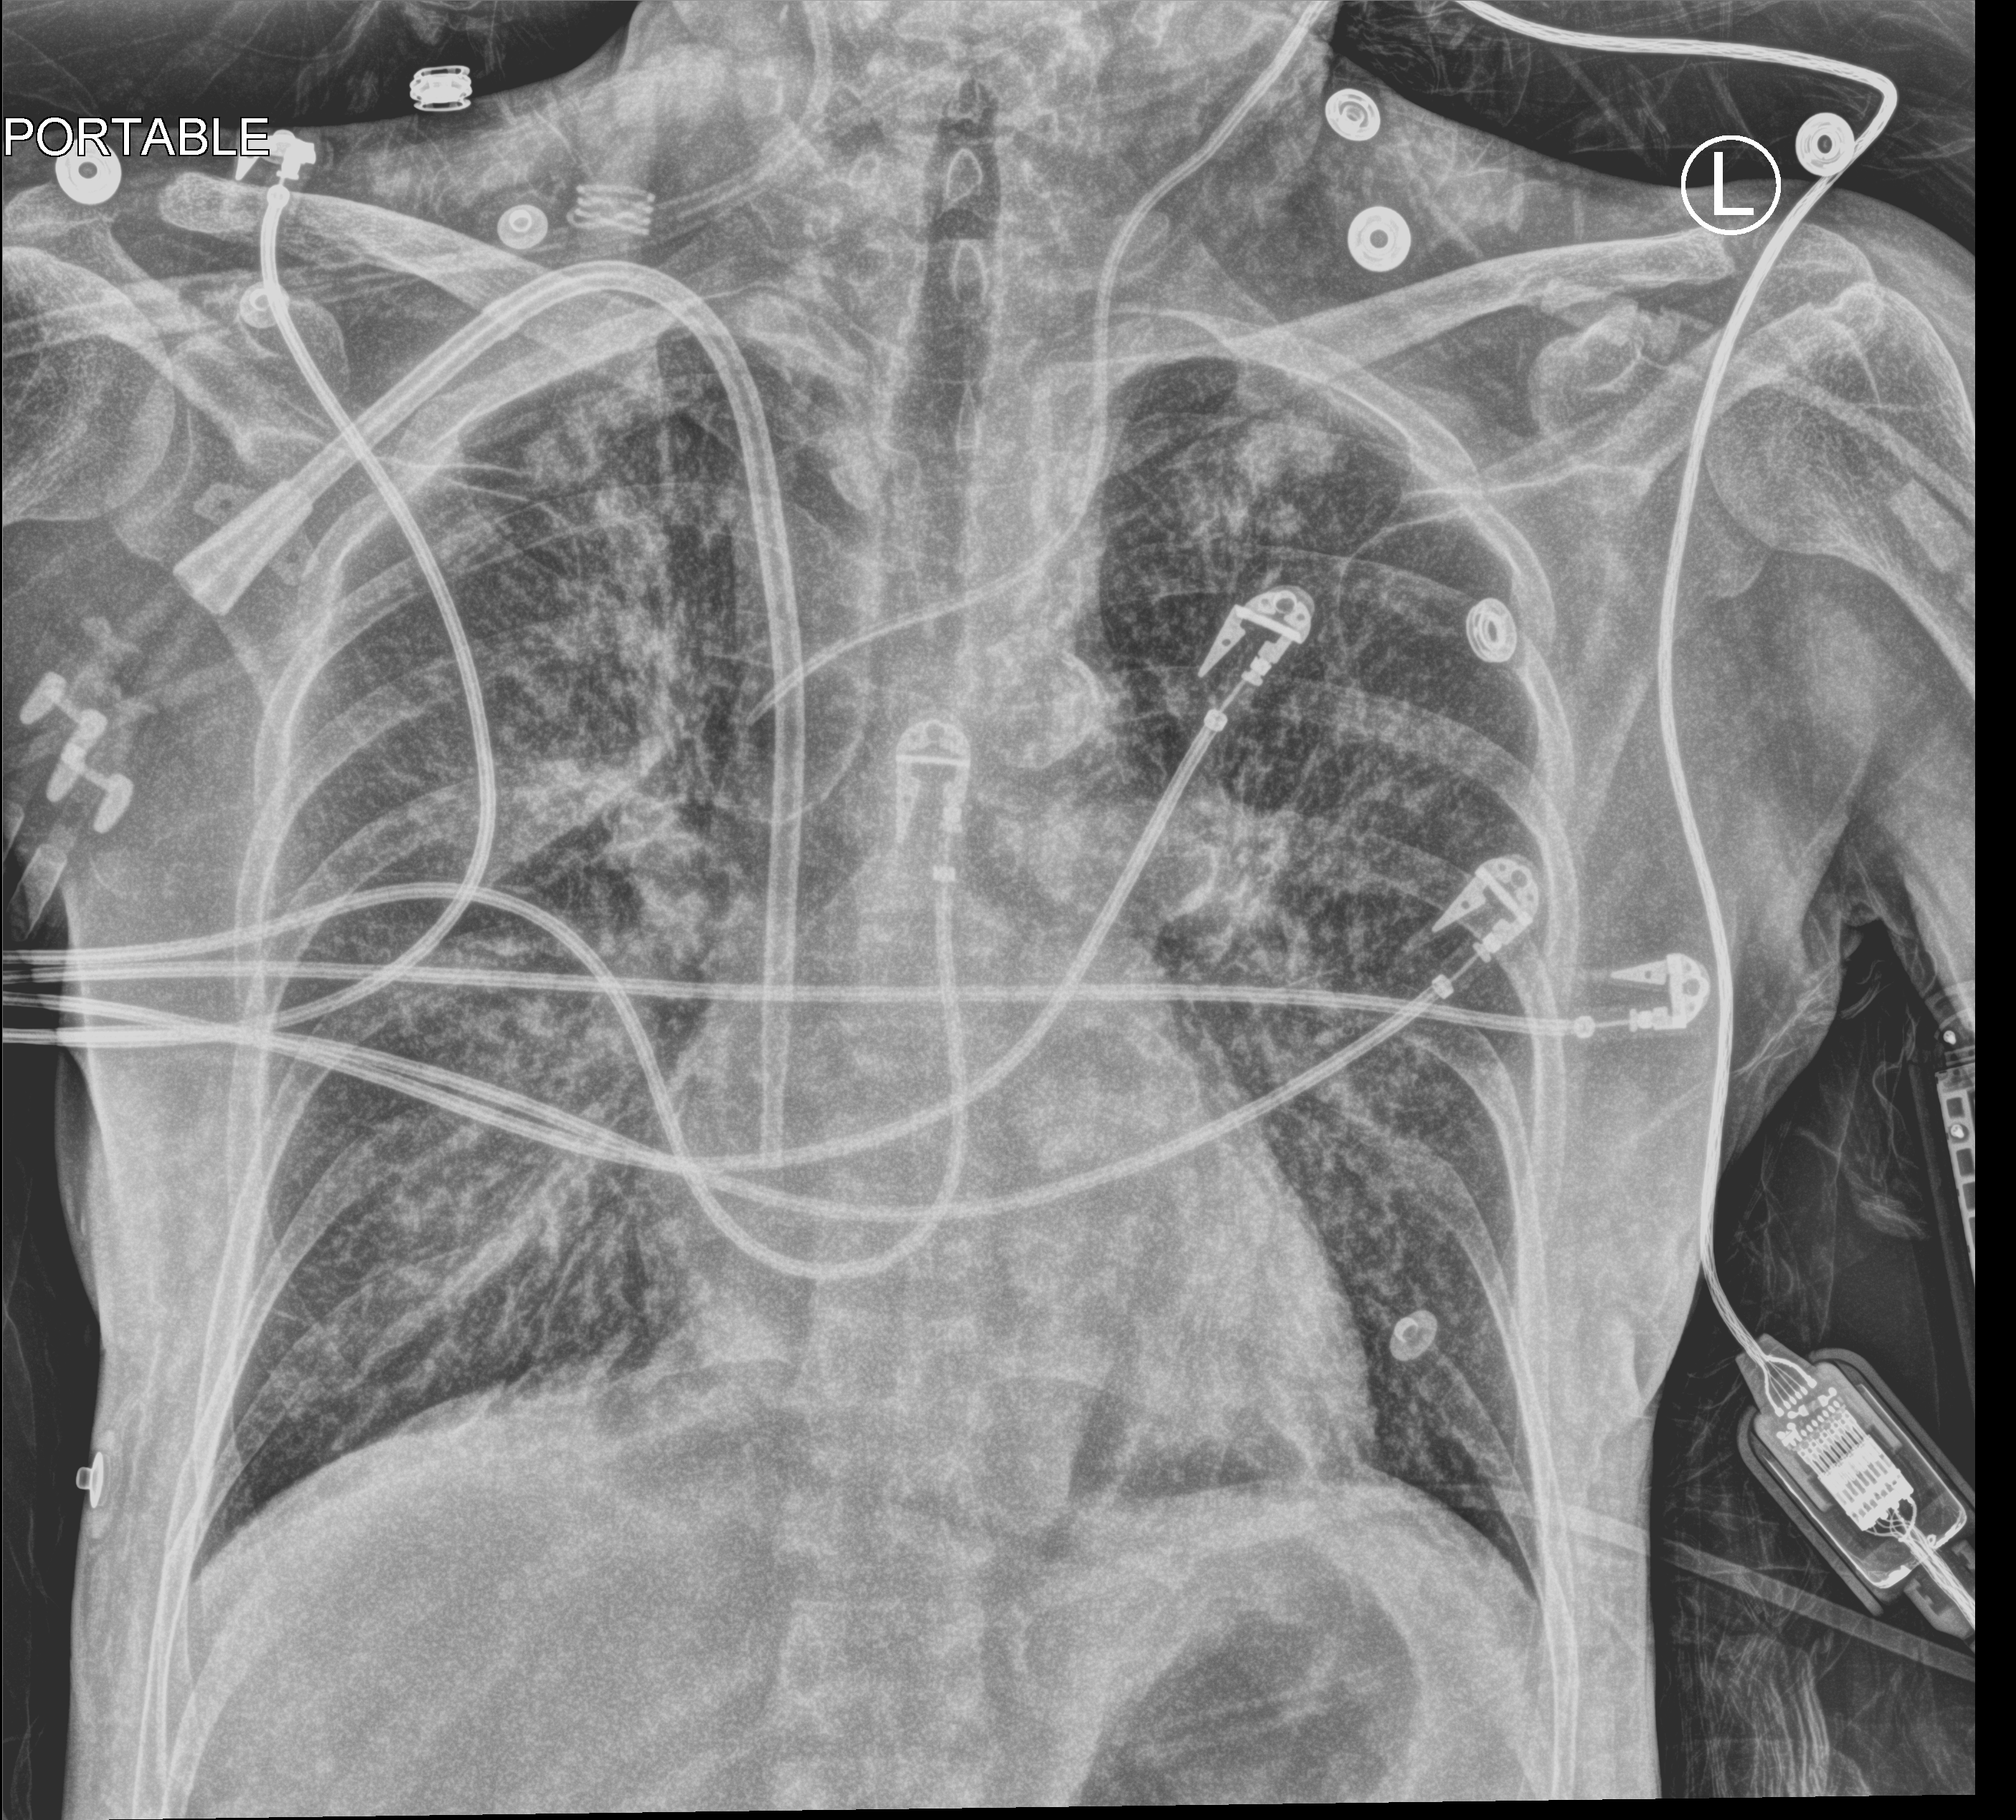
Chest X-ray (portable), anteroposterior (AP) projection. Patient hospitalised with COVID-19; female, aged 18–59 years.
Hospital-stay facts (about this admission, not read from this image; timing relative to this image not recorded): mechanically ventilated during this hospital stay: no.